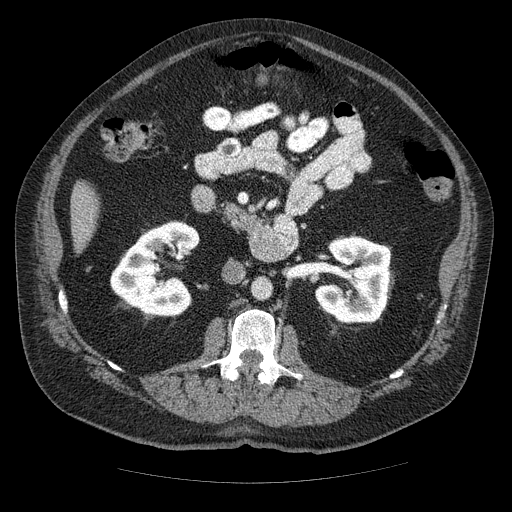
Contrast-enhanced abdominal CT (liver protocol), one axial slice; slice 8 of 85 in the series (ordered by position); reconstruction kernel STANDARD; 120 kVp; soft-tissue window (W 400 / L 40 HU); 512 × 512 image matrix, field of view 420 × 420 mm. Case-level facts recorded for this patient, not image findings: diagnosis: hepatocellular carcinoma (patient treated with transarterial chemoembolisation; whether this scan precedes or follows treatment is not stated here); TNM stage (as recorded): Stage-IIIA; Child-Pugh class: A; tumour nodularity: multinodular.
Structures marked on this image (semi-automatically segmented with operator editing):
- liver parenchyma outside the tumour (the mass and vessels are separate outlines, so this box may not span the whole liver): bounding box <70,182,98,250> (left, top, right, bottom; pixels)